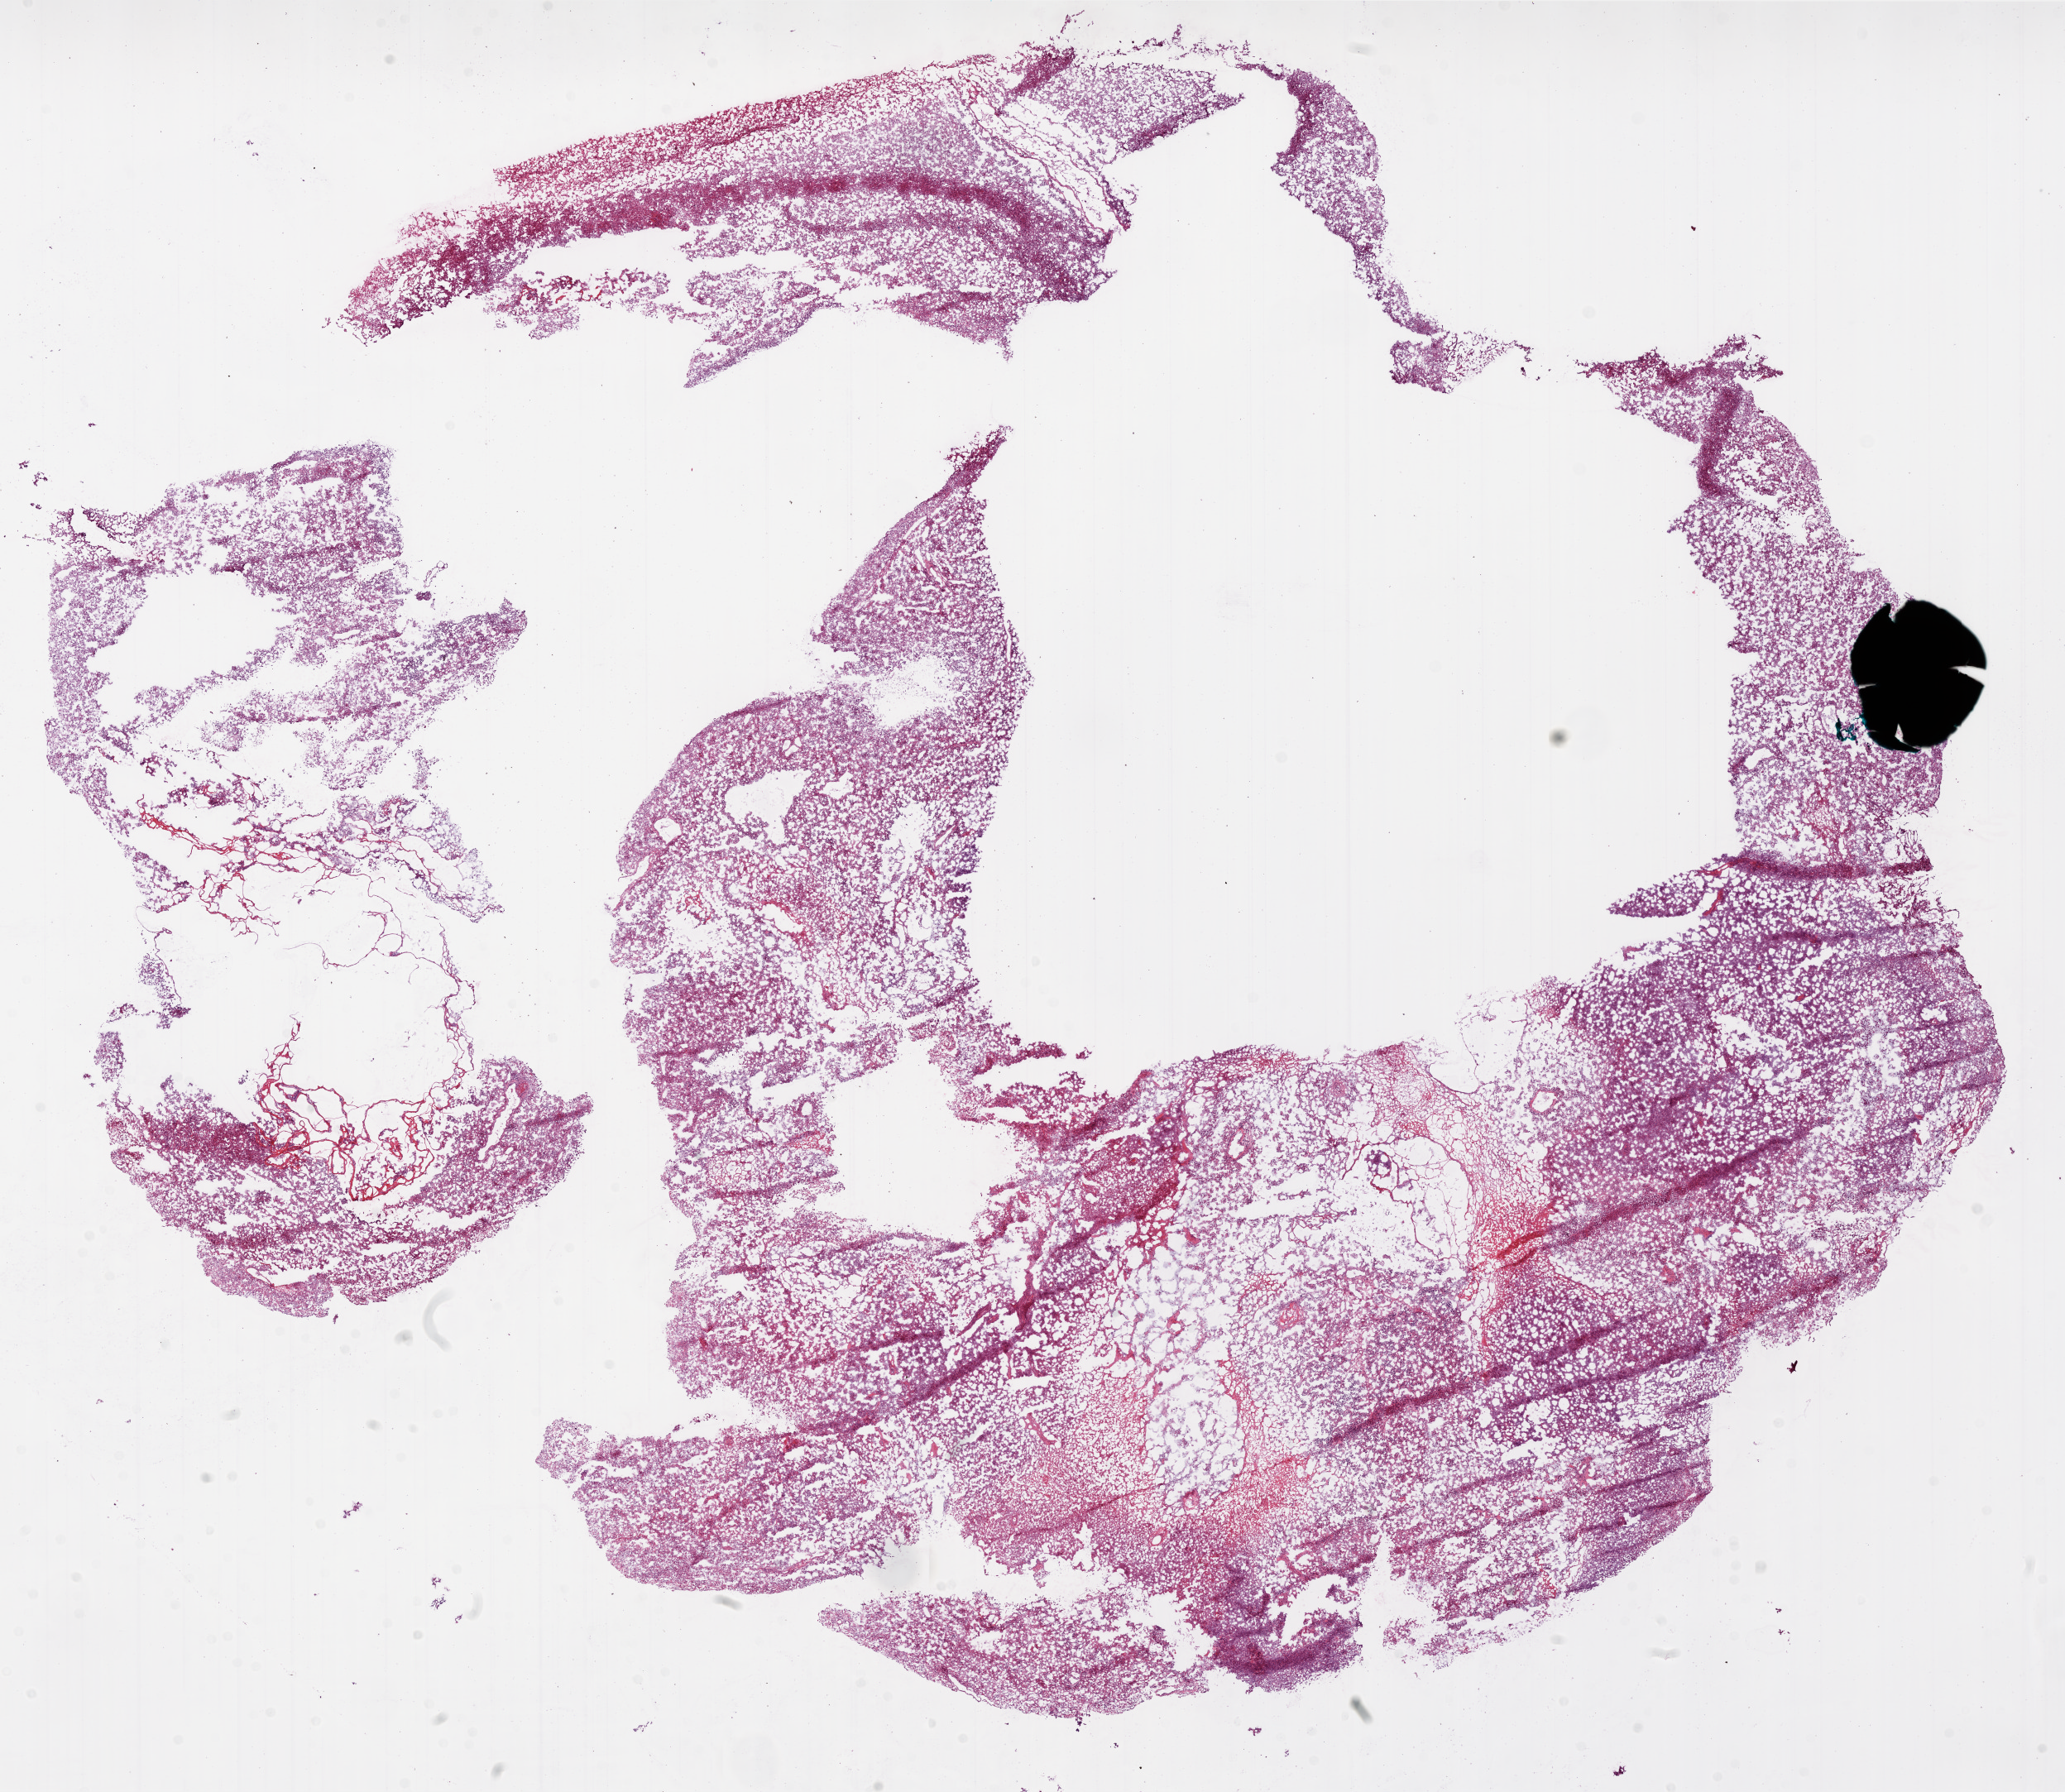
Digitized H&E tissue section (whole slide) — low-resolution overview of the scanned area, about 20.0 x 17.3 mm (slide scanned at 20x). Frozen section. Primary tumour sample from the brain. Patient: male, age at initial diagnosis 61 years. Slide review estimates, as recorded: tumour cells 70%, tumour nuclei 100%, necrosis 30%.
Histologic diagnosis: Glioblastoma.